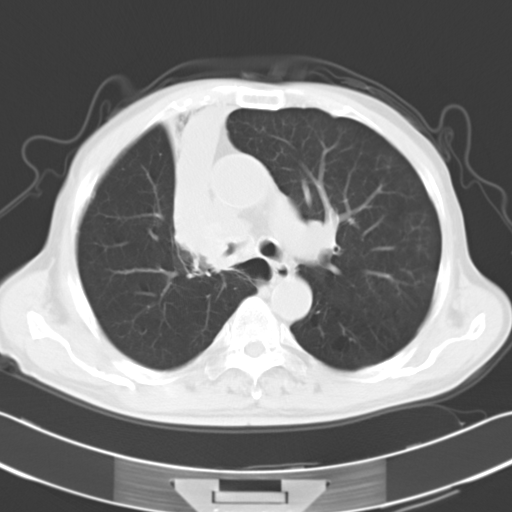
Chest CT, one axial slice; 120 kVp; lung window (W 1500 / L -600 HU); 10 mm slice thickness; 512 × 512 image matrix, field of view 339 × 339 mm. Patient: male, 73 years. Case-level facts recorded for this patient, not image findings: clinical TNM (as recorded): T2a N1 M0.
Structures marked on this image (bounding box drawn by a radiologist):
- lung tumour (recorded histology: squamous cell carcinoma): box from (x=163, y=92) to (x=231, y=266) px